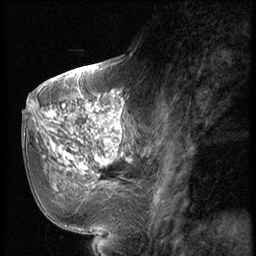
Breast MRI (dynamic contrast-enhanced), one sagittal slice; position 24 of 56 along the scan axis; dynamic contrast-enhanced series, image 2 of 2 at this slice position (ordered by acquisition); 1.5 T; TE 4.2 ms, TR 9 ms; 2.5 mm slice thickness; 256 × 256 image matrix, field of view 180 × 180 mm. Female patient, age 51 years. Case-level facts recorded for this patient, not image findings: setting: breast cancer imaged before/during neoadjuvant chemotherapy; receptor status: triple-negative.
Annotated regions visible in this slice (semi-automatically segmented with operator editing):
- analysis volume of interest (the breast-tissue region the enhancement analysis was run in; not a lesion): bounding box [x1, y1, x2, y2] px = [60, 98, 147, 197]
- tumour enhancement mask (voxels above the 140 % enhancement threshold inside the analysis volume of interest): [64, 100, 127, 187]